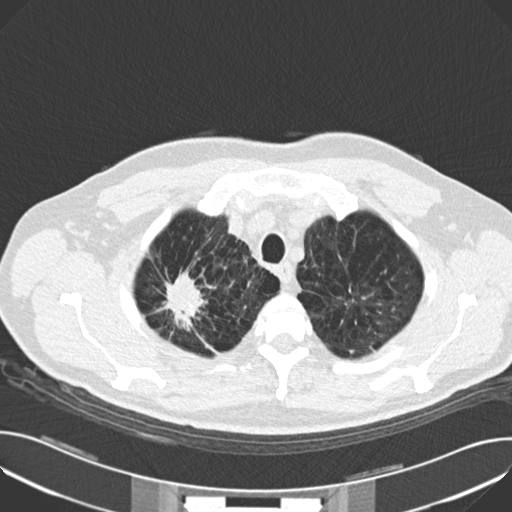
Low-dose screening chest CT, one axial slice; position 138 of 159 along the scan axis; reconstruction kernel B30f; 120 kVp; lung window (W 1500 / L -600 HU); 2 mm slice thickness; 512 × 512 image matrix, field of view 380 × 380 mm.
Annotated regions visible in this slice (manually delineated by an expert):
- lesion 1 (tumor, upper lobe of right lung): box from (x=167, y=272) to (x=204, y=323) px